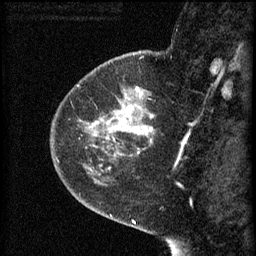
Breast MRI (dynamic contrast-enhanced), one sagittal slice; slice 17 of 60 in the series (ordered by position); 3 images stored at this slice position (order not interpretable as contrast timing); 1.5 T; TE 4.2 ms, TR 8.2 ms; 256 × 256 image matrix, field of view 180 × 180 mm. Female patient, age 44 years.
Outlined on this slice (semi-automatic segmentation, software-assisted and operator-edited):
- analysis volume of interest (the breast-tissue region the enhancement analysis was run in; not a lesion): bounding box <73,82,155,165> (left, top, right, bottom; pixels)
- tumour enhancement mask (voxels above the 70 % enhancement threshold inside the analysis volume of interest): <87,88,155,155>